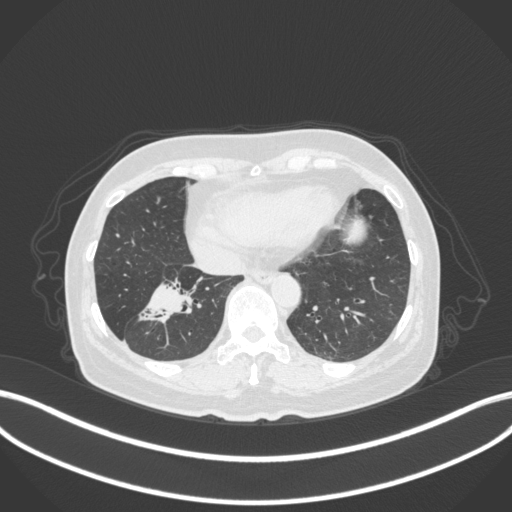
Chest CT, one axial slice; slice 118 of 429 in the series (ordered by position); reconstruction kernel B31f; lung window (W 1500 / L -600 HU); 512 × 512 image matrix. Female patient, age 67 years. Case-level facts recorded for this patient, not image findings: clinical TNM (as recorded): T1c N1 M0.
Outlined on this slice (rectangle marked by the reading radiologist):
- lung tumour (recorded histology: adenocarcinoma): bounding box (x1, y1, x2, y2) in pixels: (133, 273, 210, 328)